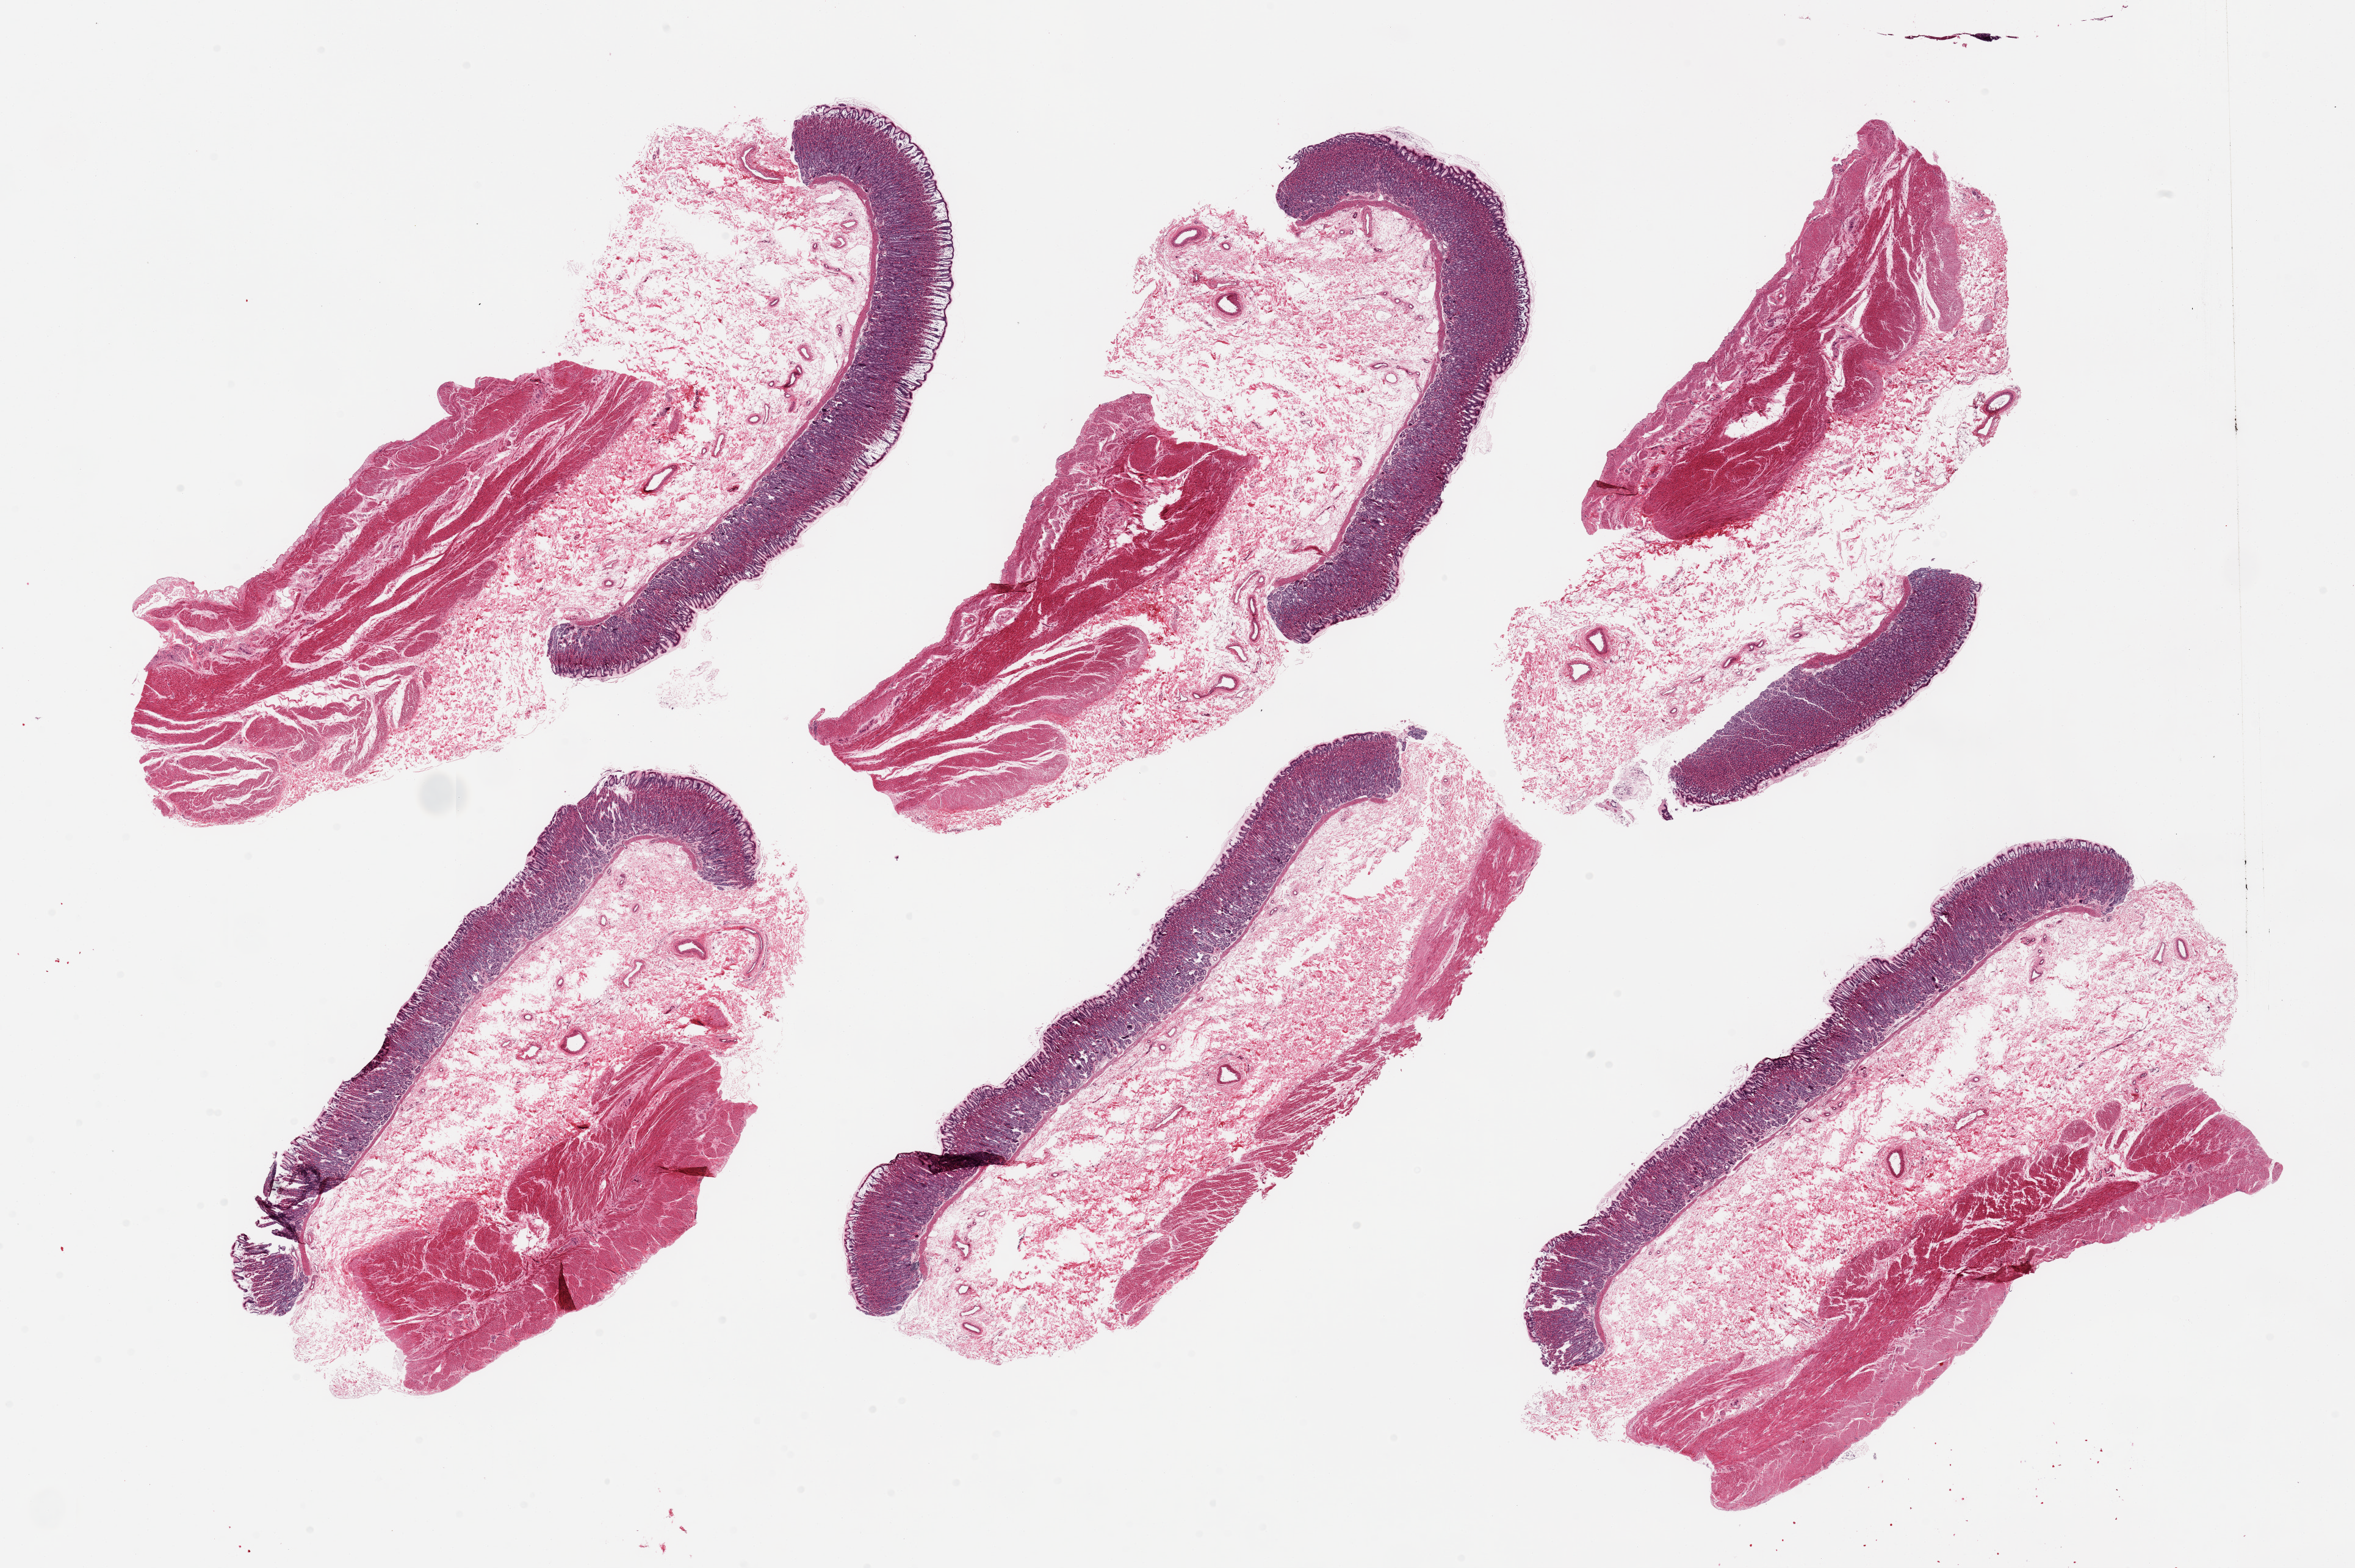
Haematoxylin and eosin whole-slide image, whole scanned area (about 30.5 x 20.3 mm) shown as a low-resolution overview; PAXgene-fixed paraffin-embedded (PFPE) section; section of stomach (target tissue); tissue donor sample. Female donor.
Reviewer comment on this tissue sample: 6 pieces, well-preserved mucosa up to ~1mm, ~20% thickness.